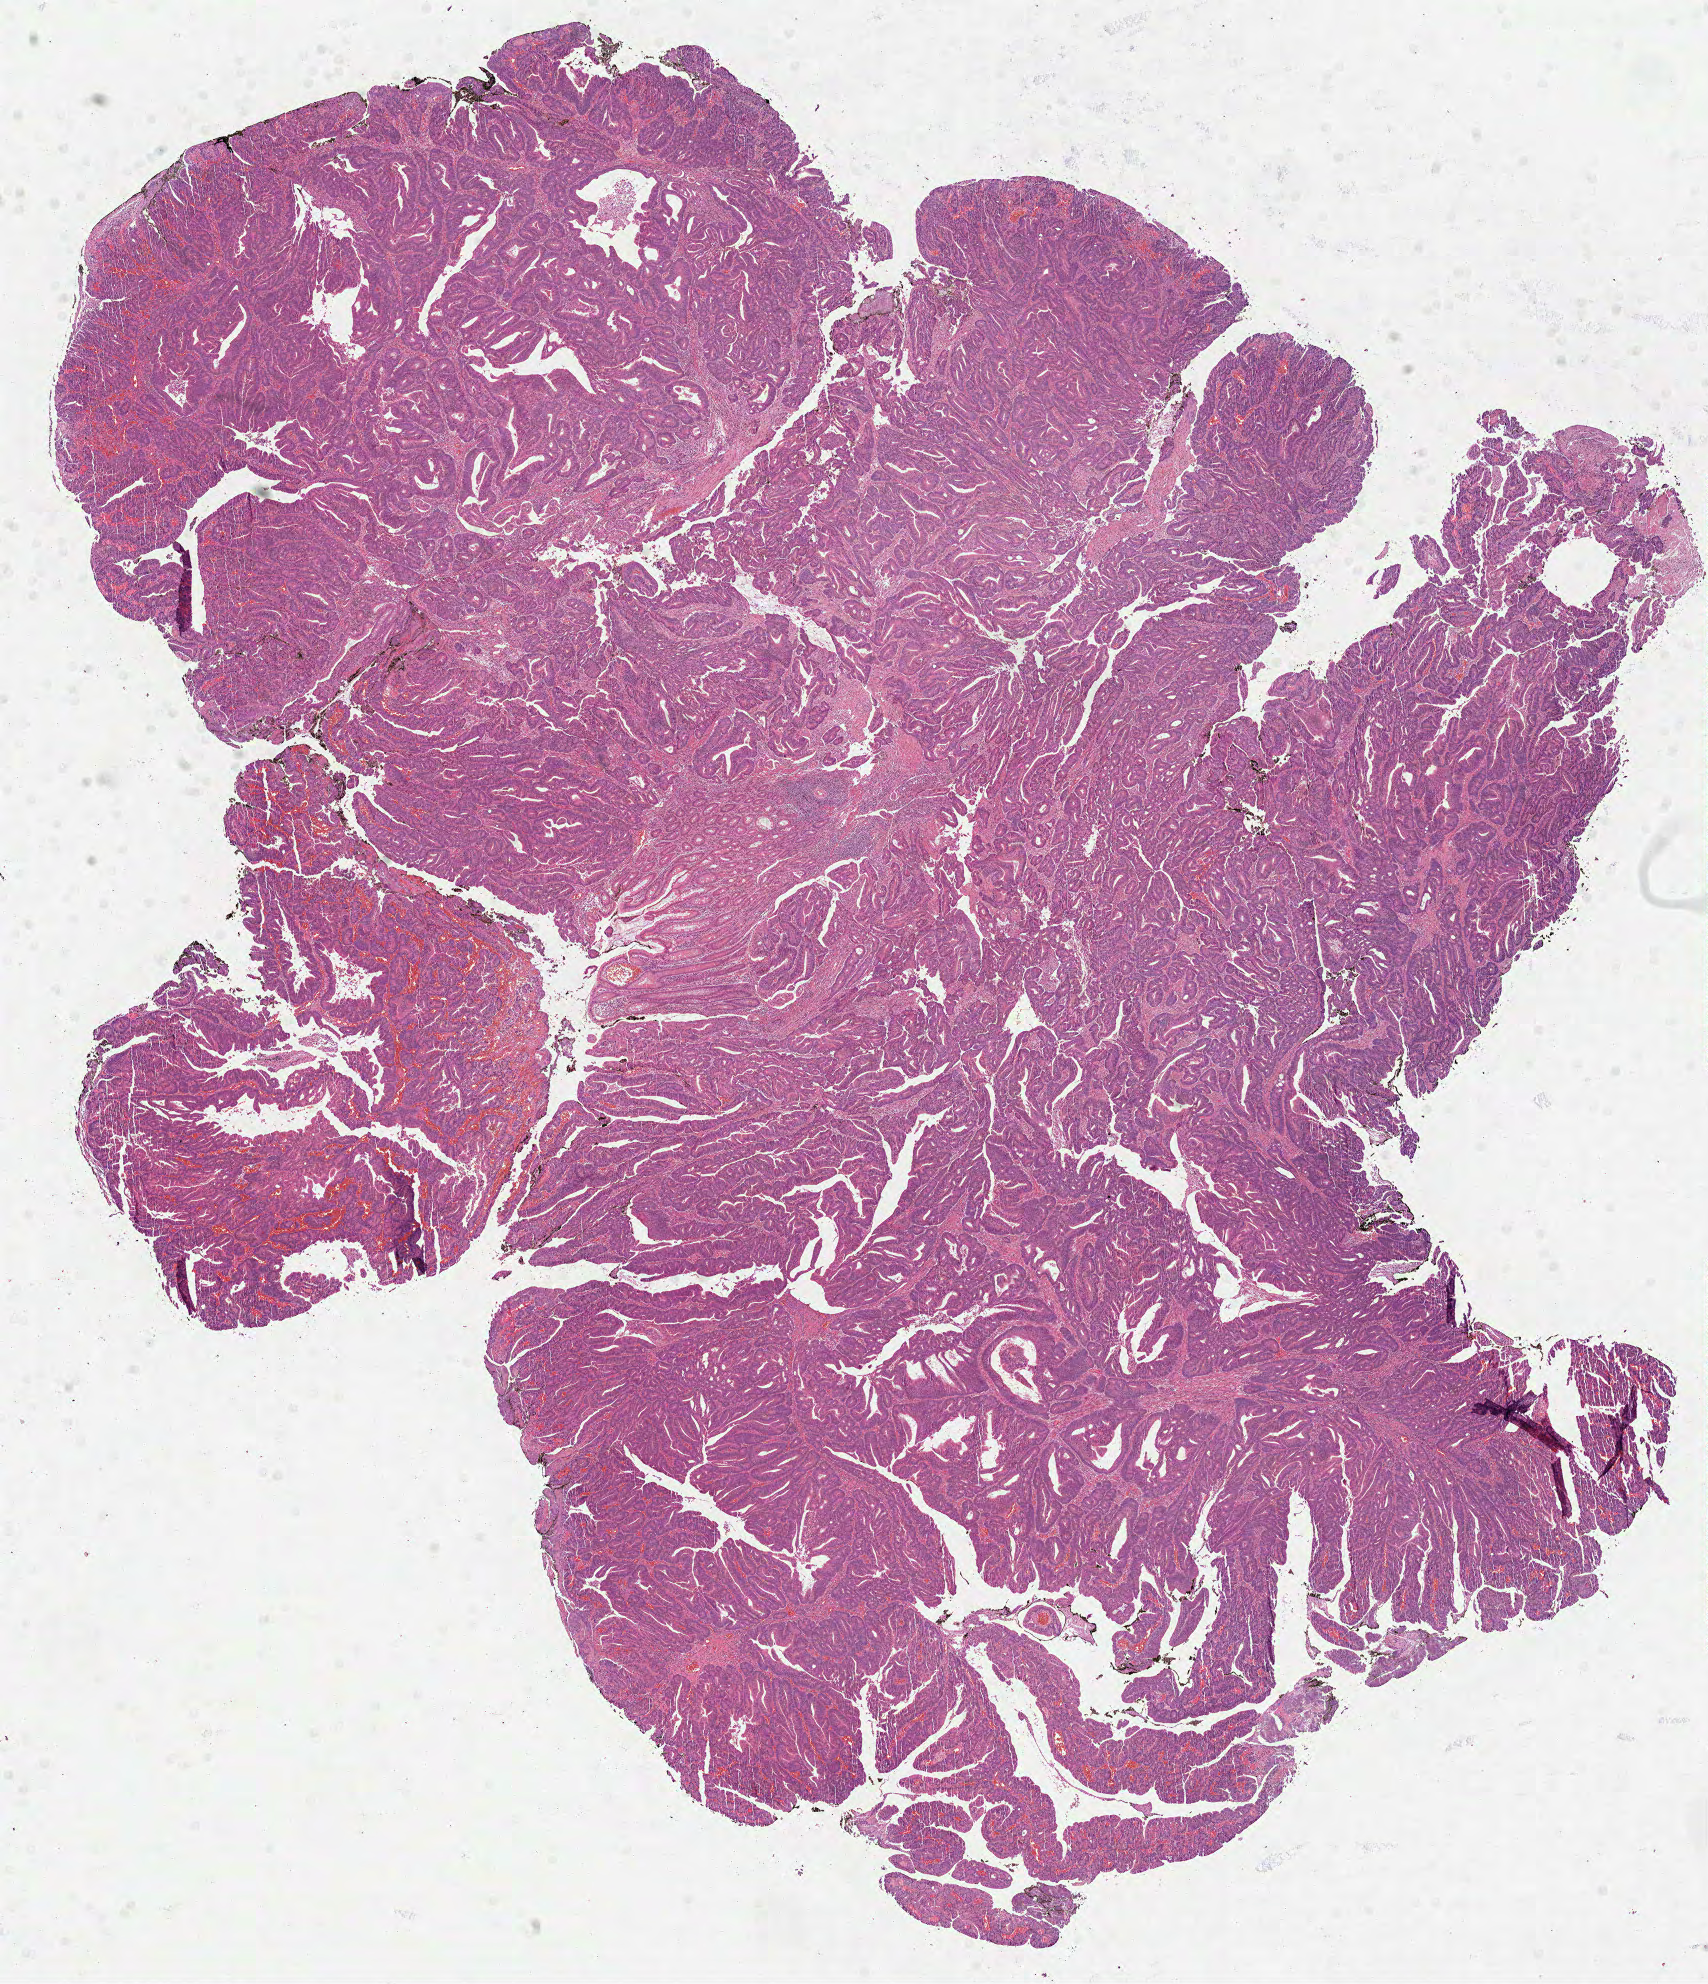
Hematoxylin and eosin (H&E) stained whole-slide image, a low-resolution overview of the entire scanned area, about 13.8 x 16.0 mm. Formalin-fixed paraffin-embedded (FFPE) diagnostic section. Primary tumour sample from the colon. Patient: male, age at initial diagnosis 76 years.
Diagnosis: Adenocarcinoma, NOS (ascending colon).